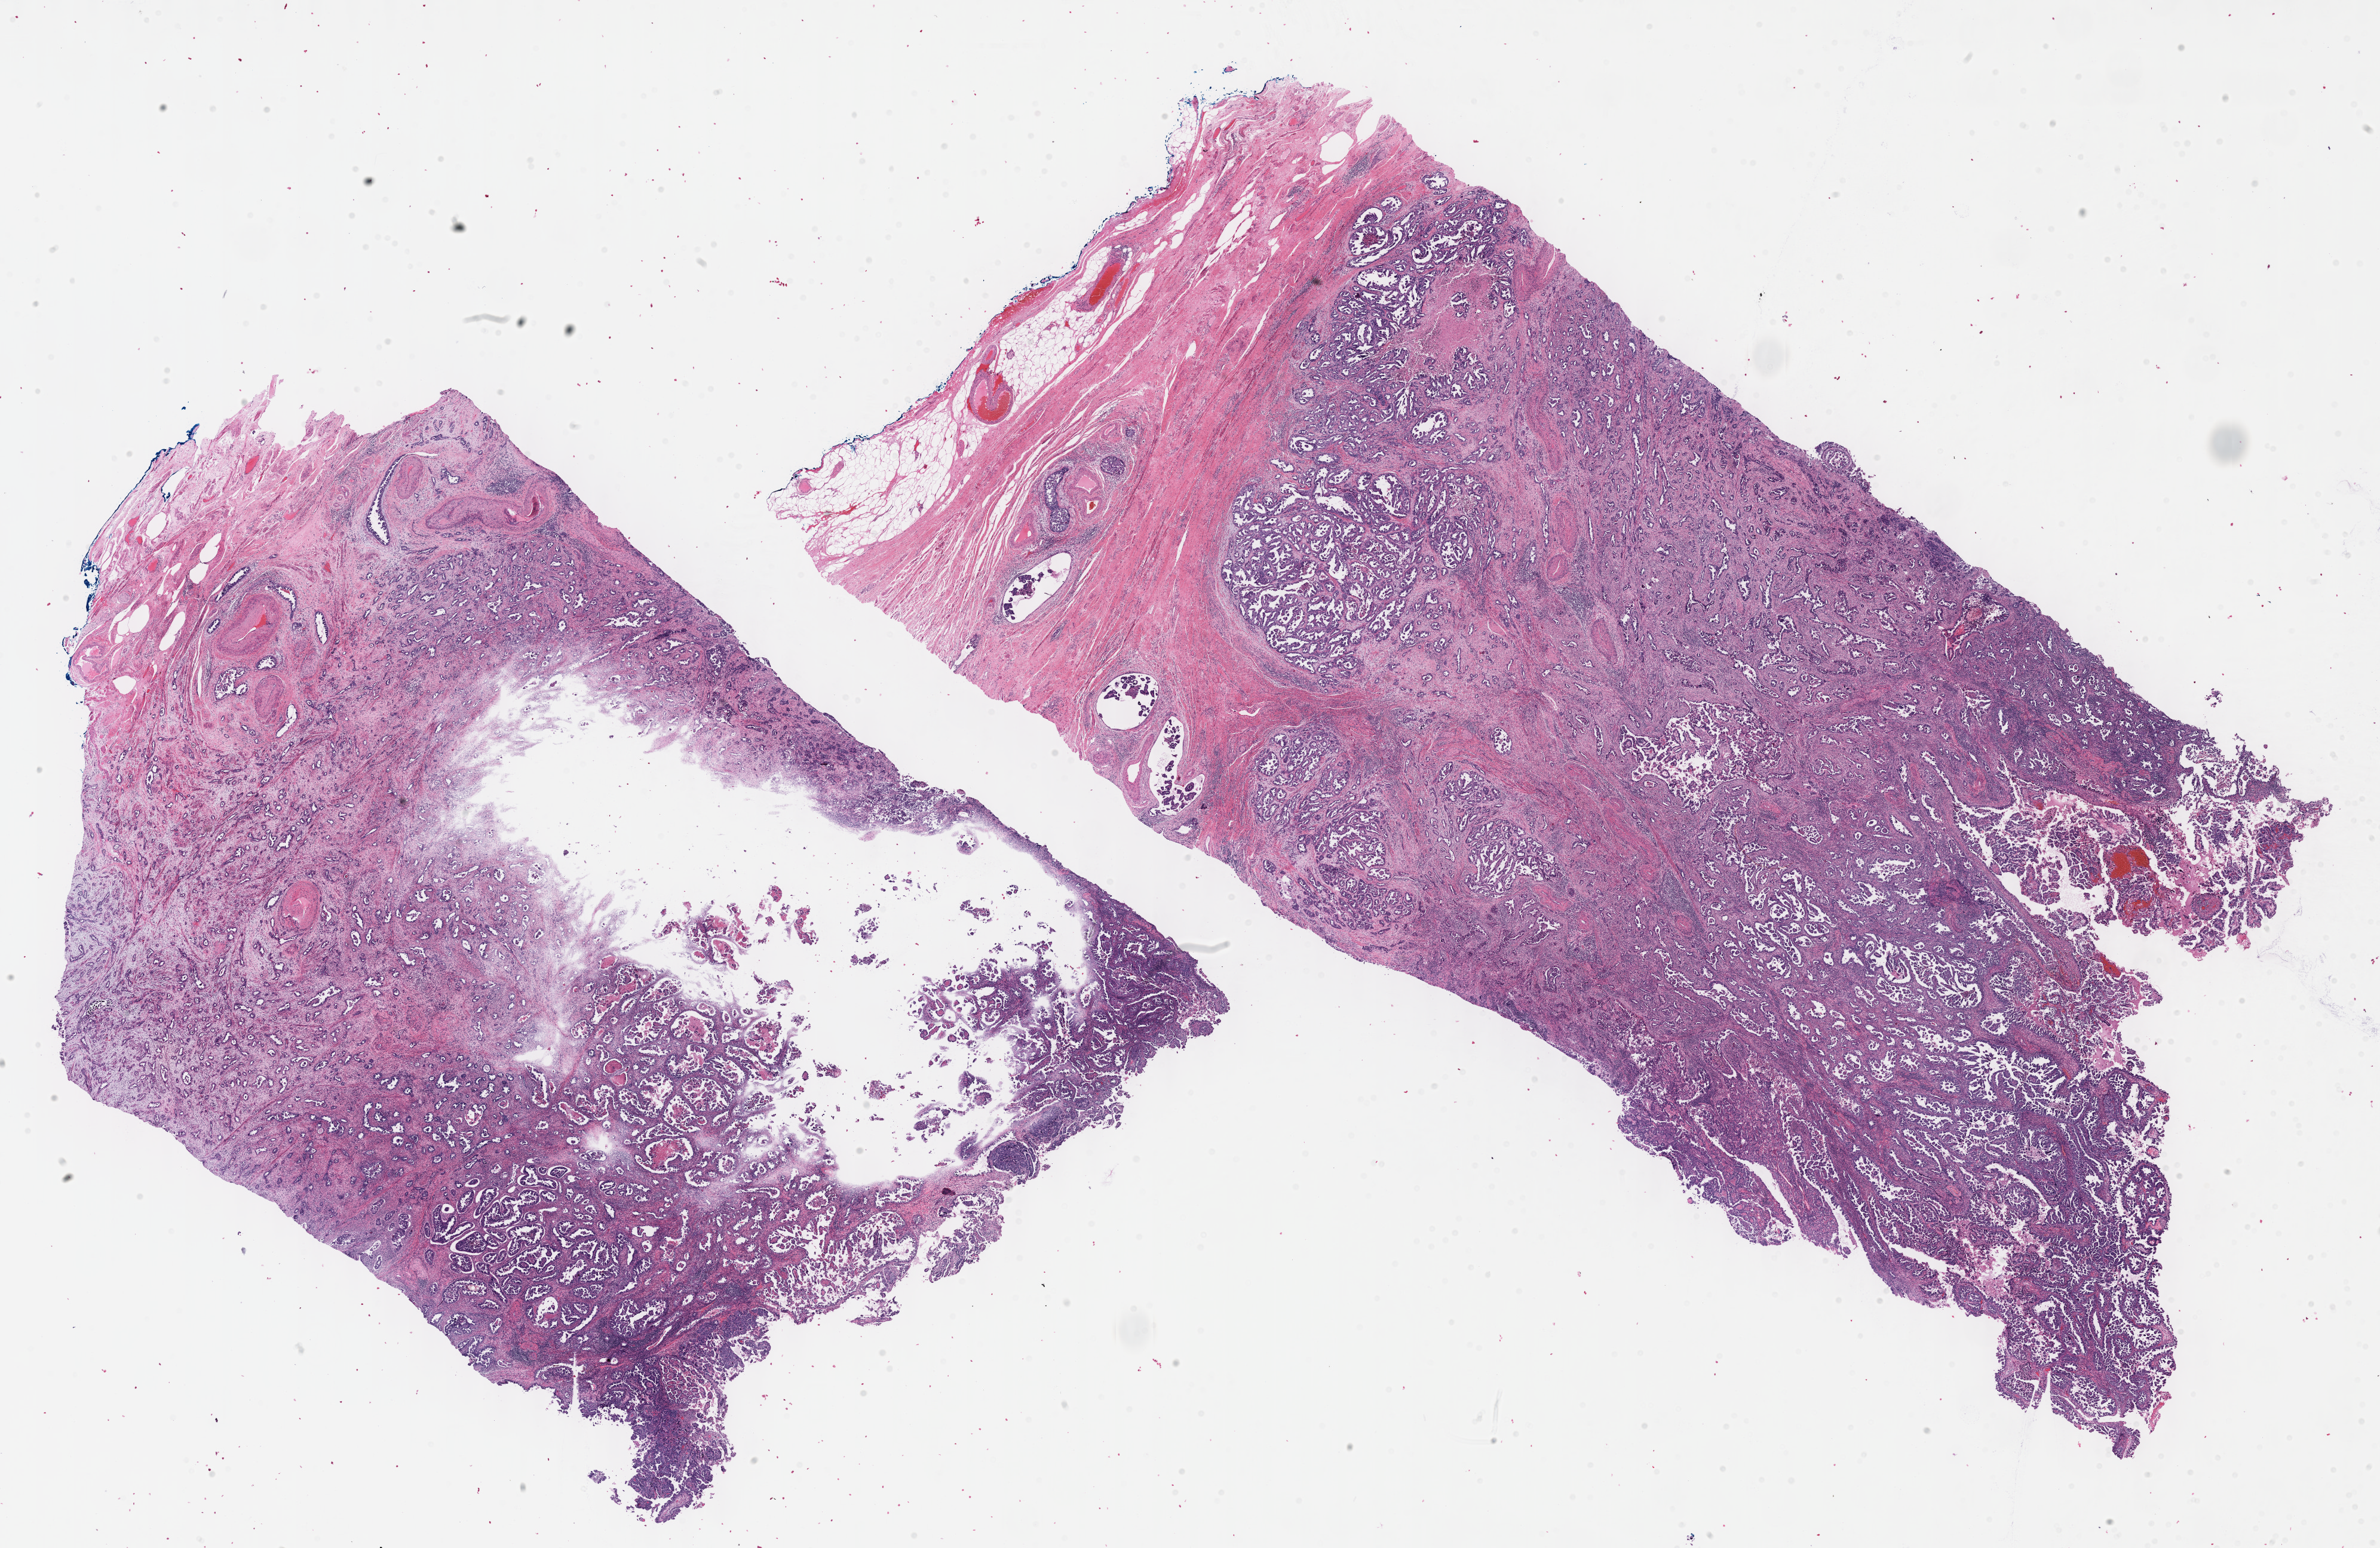
H&E whole-slide image — low-resolution overview of the scanned area, about 32.2 x 20.9 mm, formalin-fixed paraffin-embedded (FFPE) diagnostic section, primary tumour sample from the uterus. Female, age 68 years at initial diagnosis.
Histologic diagnosis: Serous cystadenocarcinoma, NOS (endometrium).